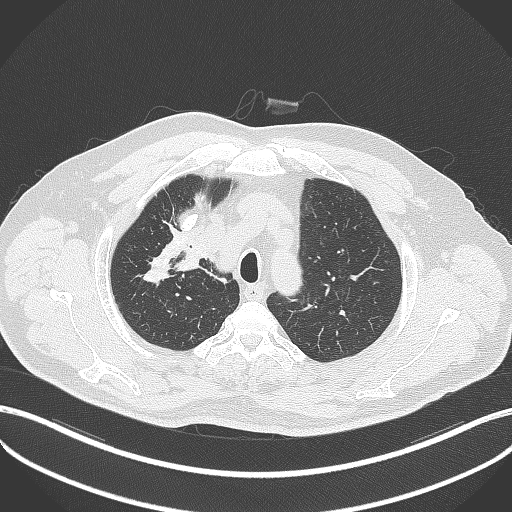
Chest CT, one axial slice; position 315 of 411 along the scan axis; reconstruction kernel B70f; 120 kVp; lung window (W 1500 / L -600 HU); 1 mm slice thickness; 512 × 512 image matrix. Male patient, age 60 years. Case-level facts recorded for this patient, not image findings: clinical TNM (as recorded): T1b N1 M0.
Structures marked on this image (rectangle marked by the reading radiologist):
- lung tumour (recorded histology: squamous cell carcinoma): bounding box <178,249,208,275> (left, top, right, bottom; pixels)